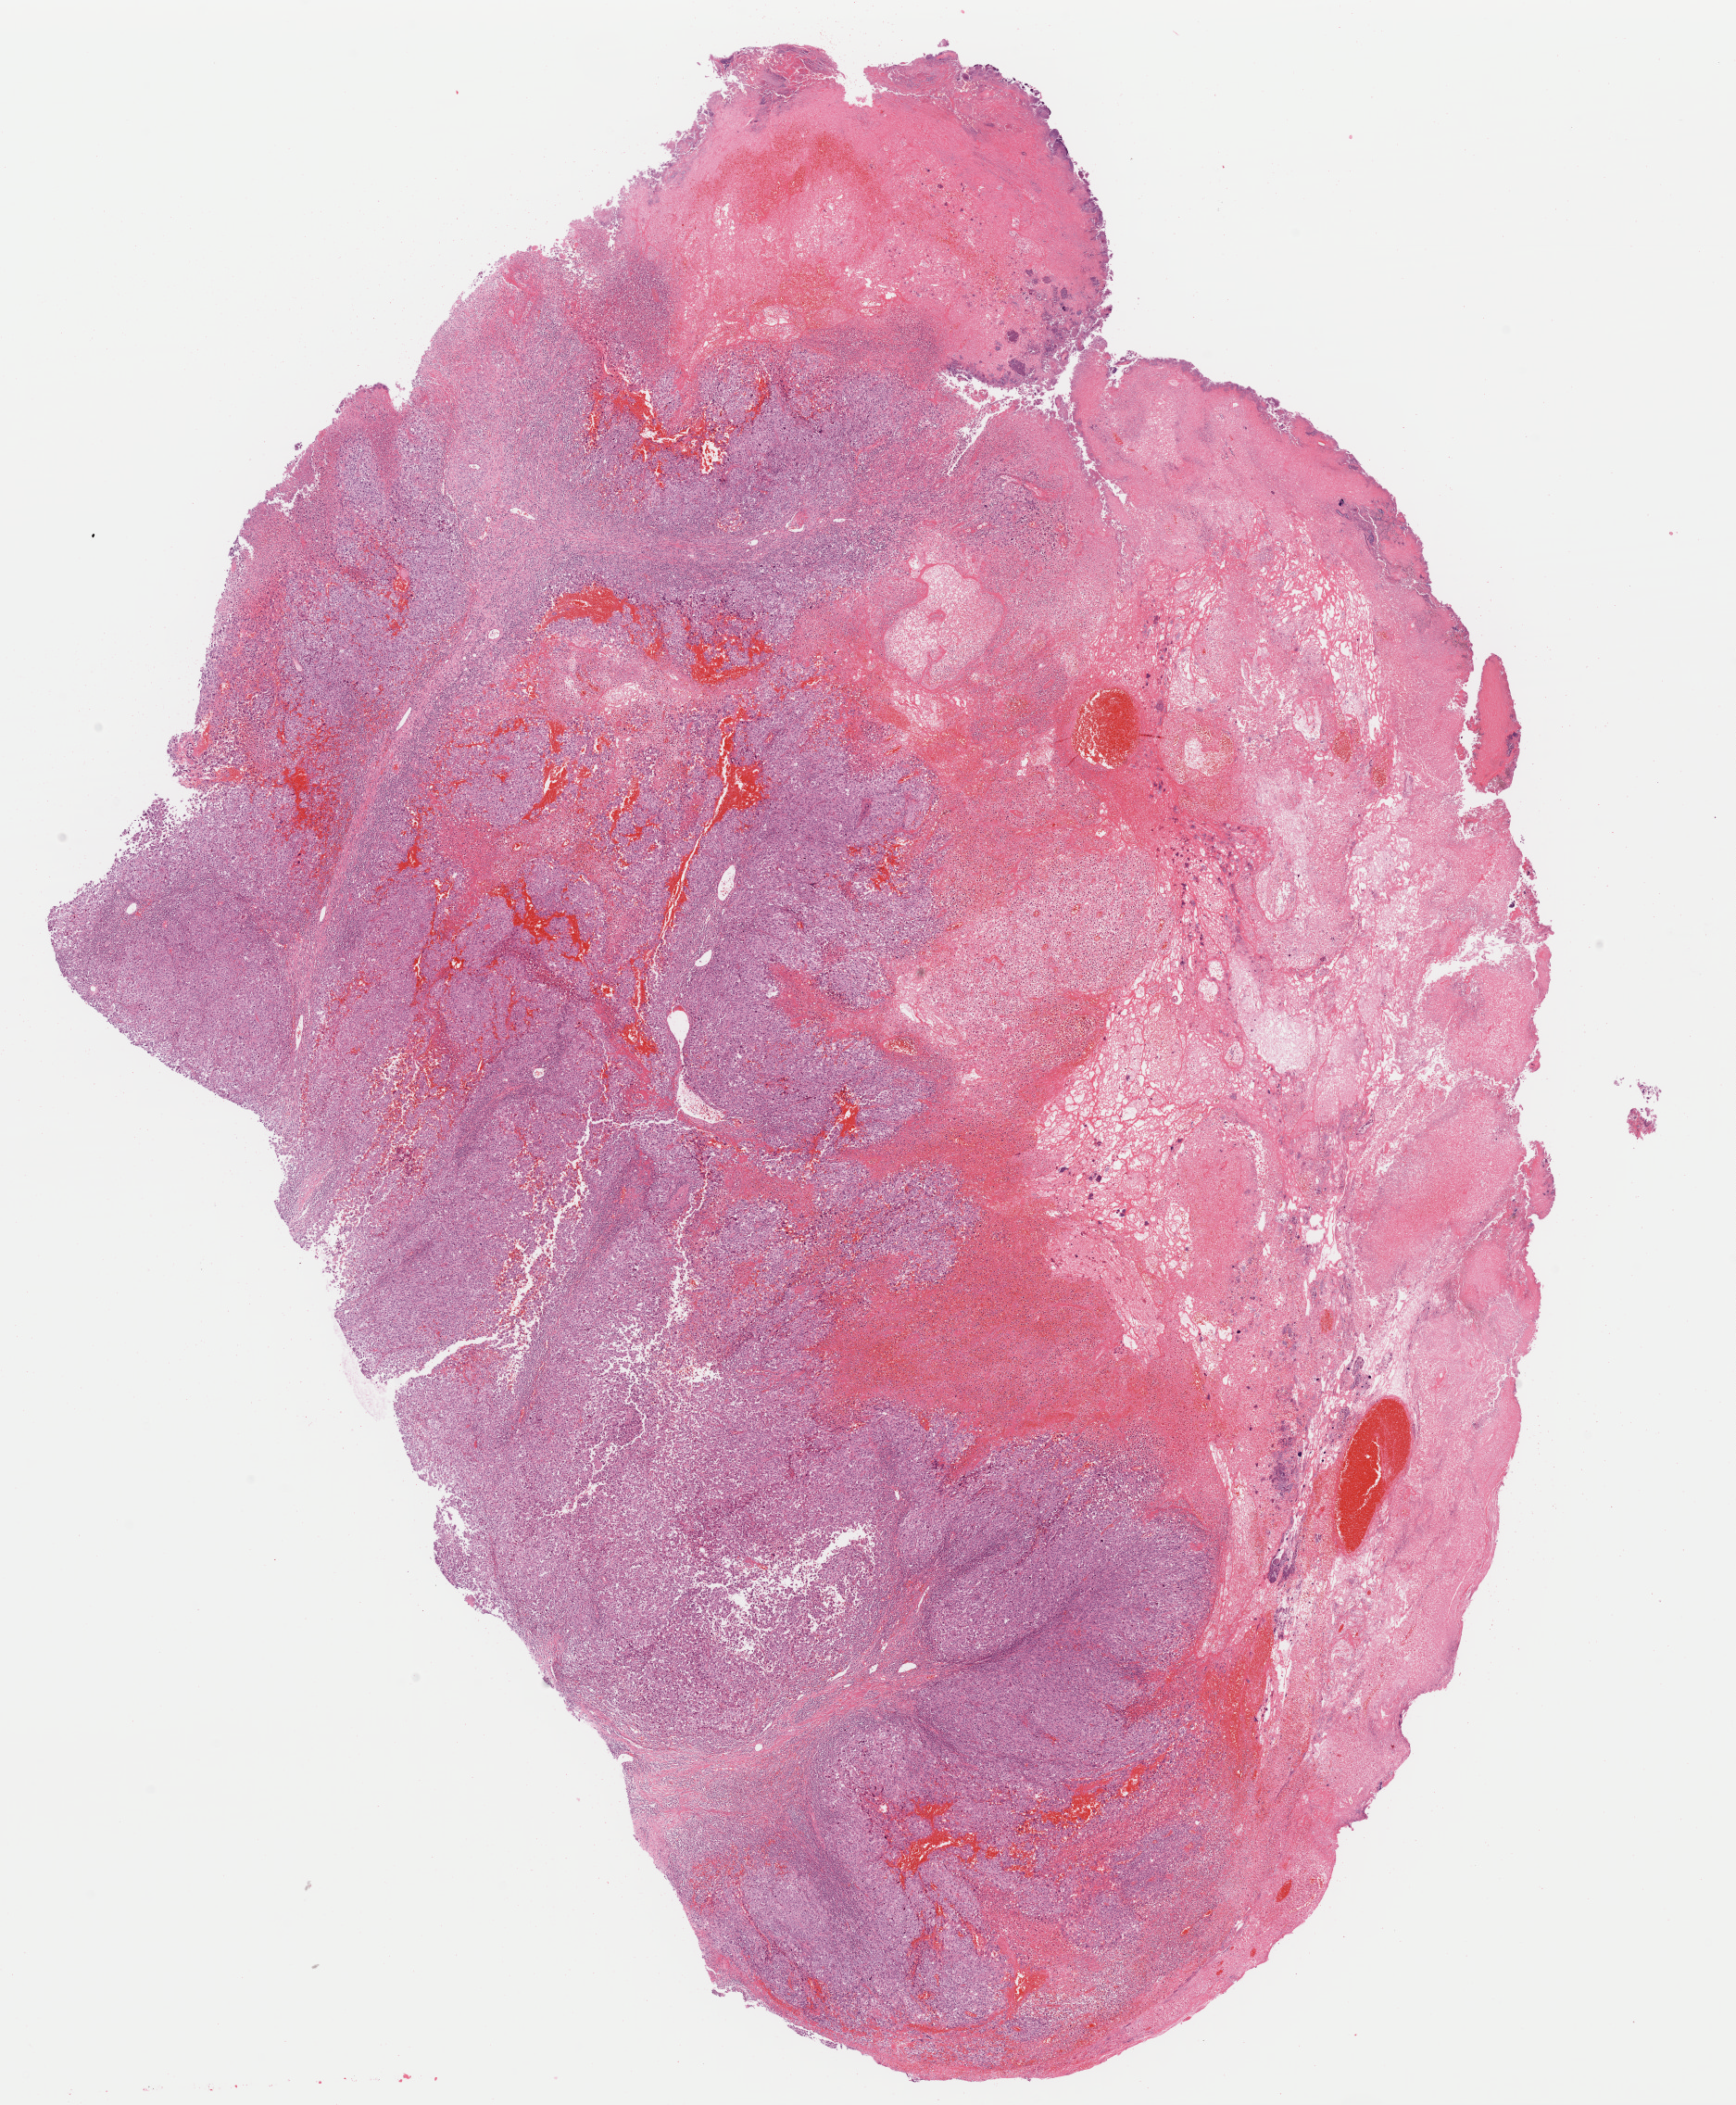
Digitized H&E tissue section (whole slide) — whole scanned area (about 14.8 x 17.9 mm, slide scanned at 40x) shown as a low-resolution overview; FFPE section; primary tumour sample from the head and neck. Male patient; age at initial diagnosis 73 years. Histologic grade: G3 (poorly differentiated).
• pathologic diagnosis: Squamous cell carcinoma, NOS (cheek mucosa)
• AJCC pathologic stage: II